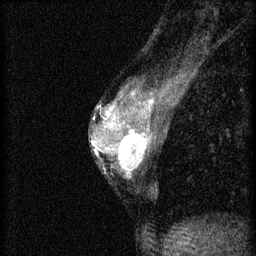
Breast MRI (dynamic contrast-enhanced), one sagittal slice. Slice 29 of 46 in the series (ordered by position). 3 images stored at this slice position (order not interpretable as contrast timing). 1.5 T. TE 4.2 ms, TR 8.2 ms. 2 mm slice thickness. 256 × 256 image matrix, field of view 180 × 180 mm. Female patient, age 44 years.
Outlined on this slice (semi-automatically segmented with operator editing):
- analysis volume of interest (the breast-tissue region the enhancement analysis was run in; not a lesion): box from (x=110, y=128) to (x=156, y=177) px
- tumour enhancement mask (voxels above the 70 % enhancement threshold inside the analysis volume of interest): (x=115, y=128)–(x=153, y=175)